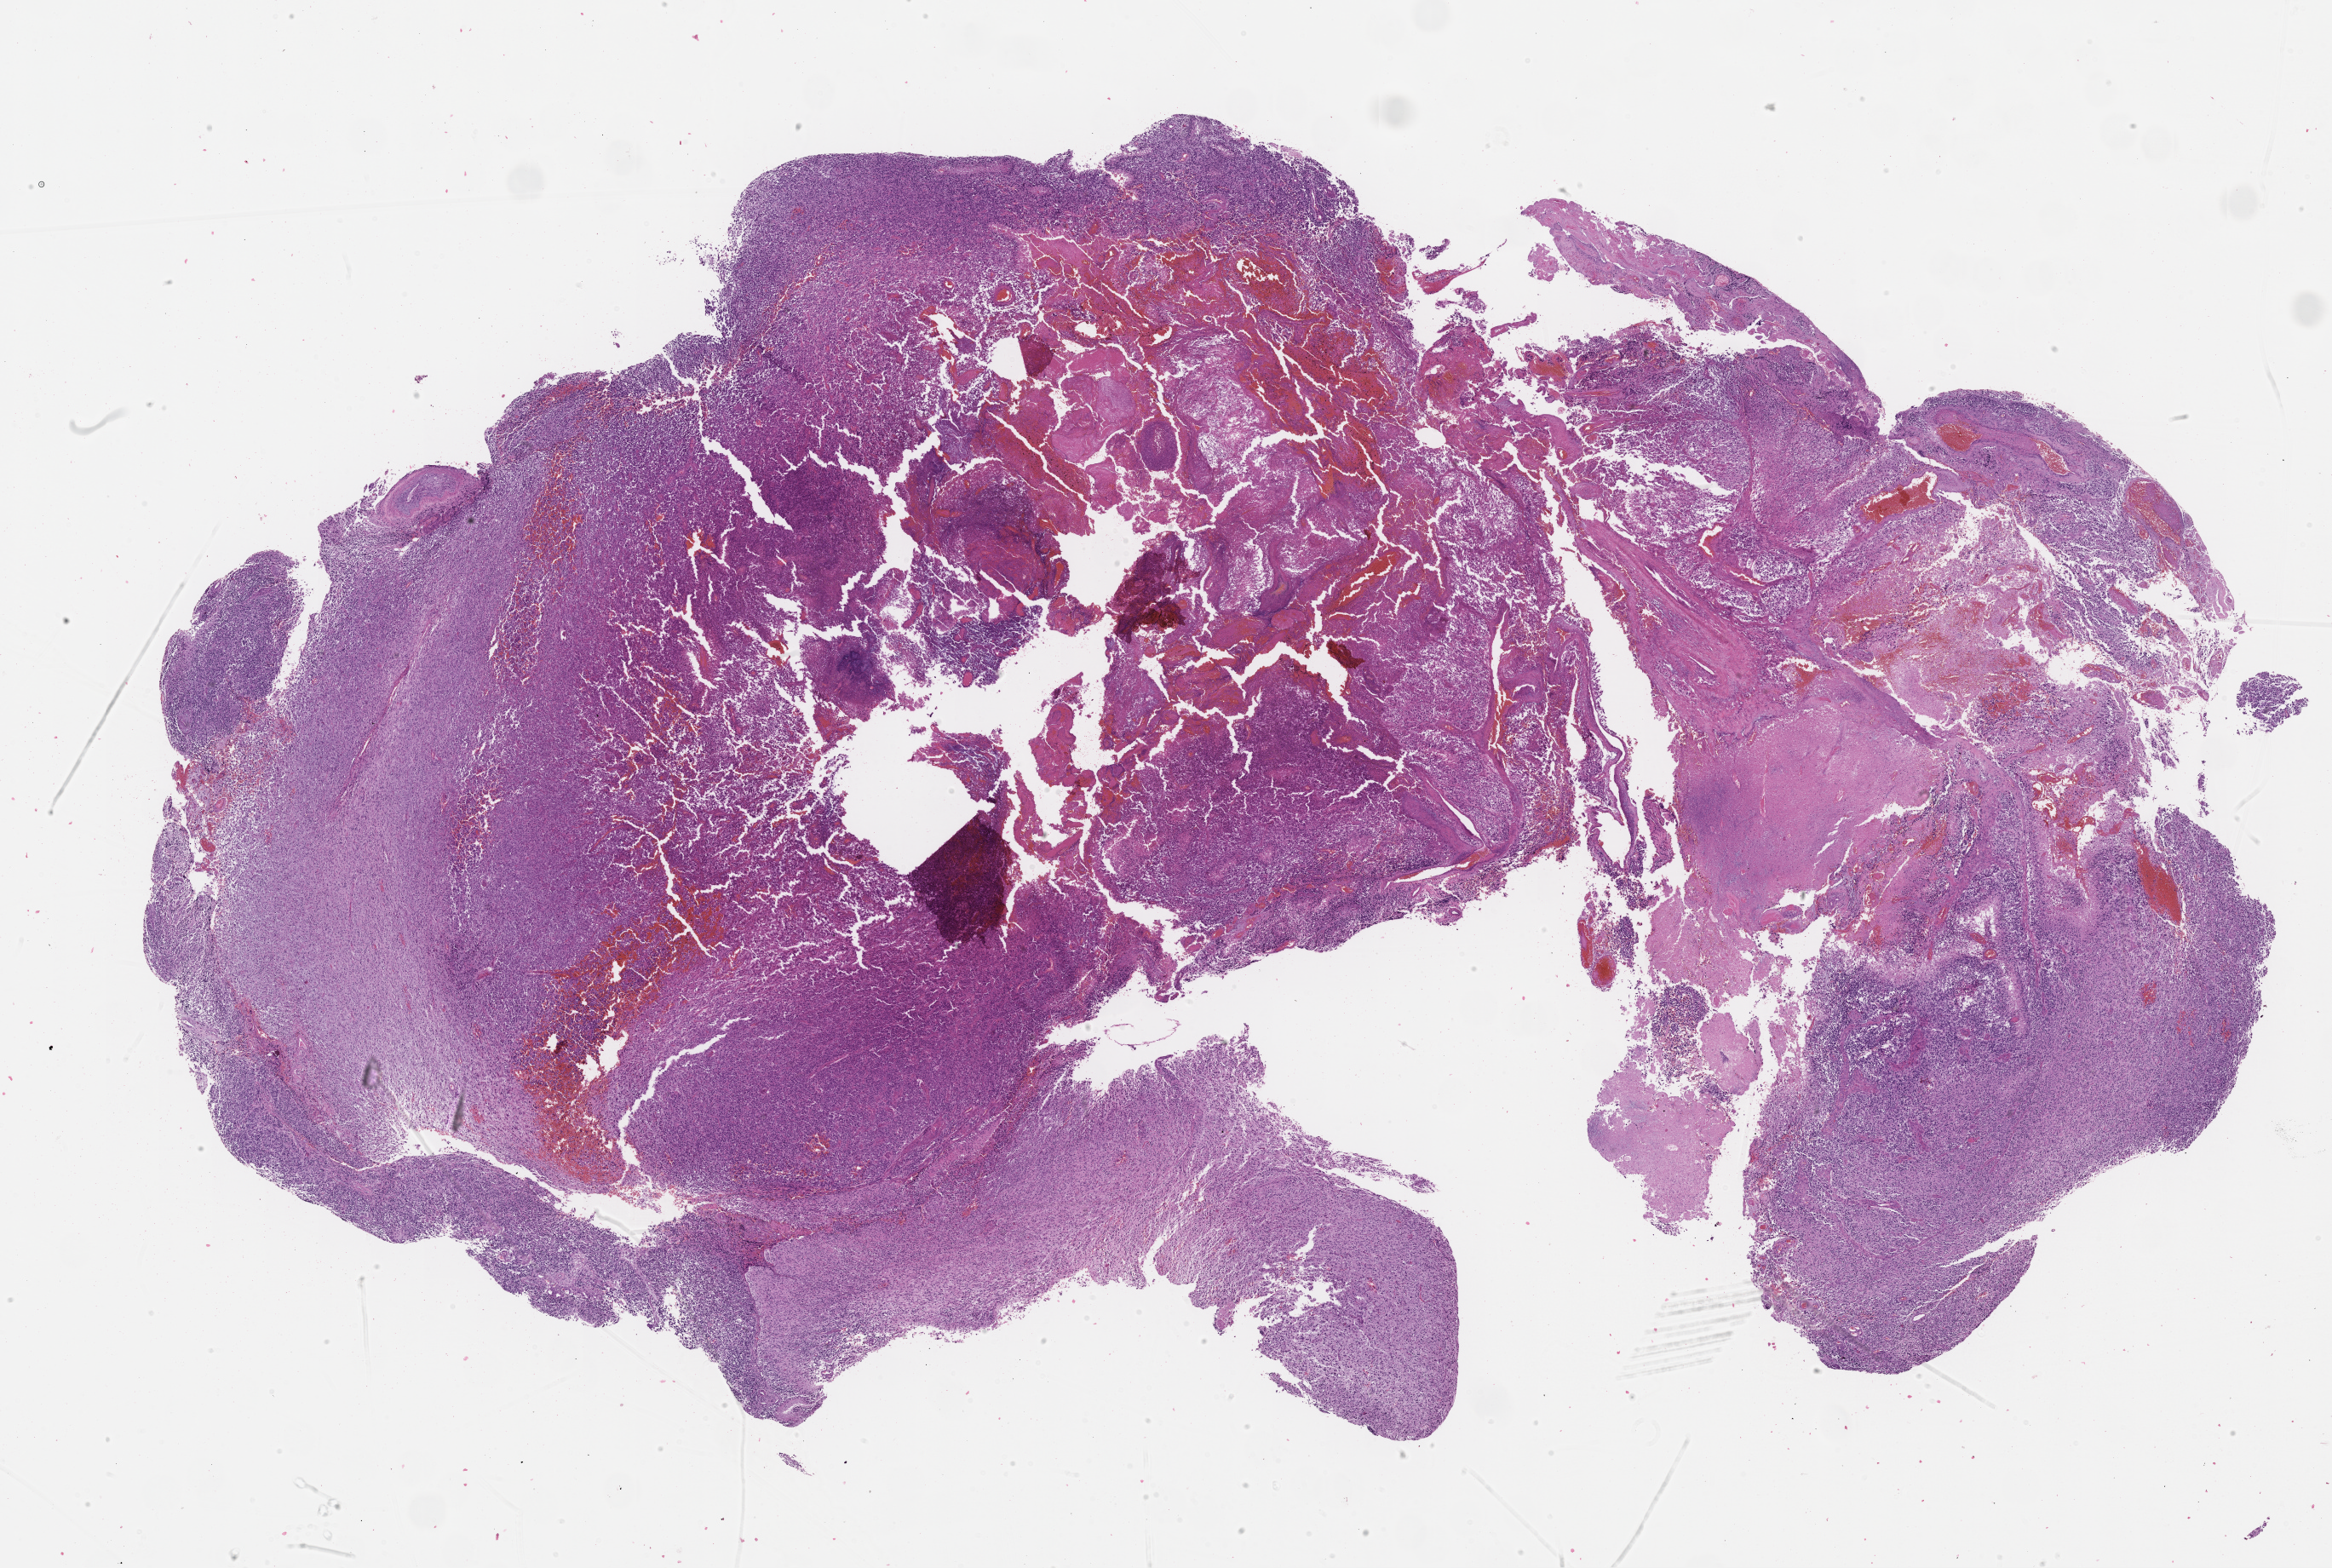
Hematoxylin and eosin (H&E) stained whole-slide image — whole scanned area (about 22.2 x 14.9 mm, slide scanned at 40x) shown as a low-resolution overview; formalin-fixed paraffin-embedded (FFPE) diagnostic section; primary tumour sample from the brain. Female patient; age at initial diagnosis 78 years.
Pathologic diagnosis: Glioblastoma.